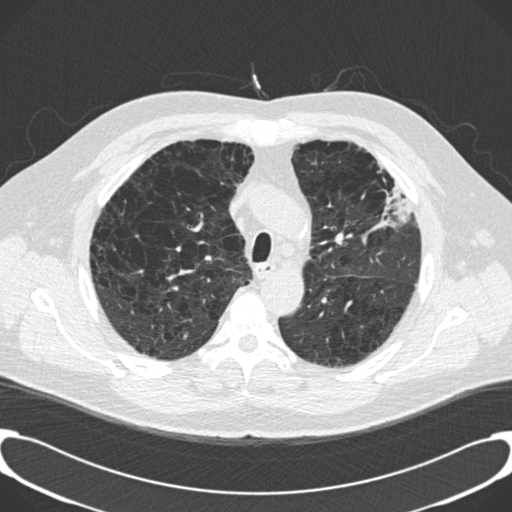
Axial slice from a low-dose chest CT screening exam; third screening round (two years after baseline); lung window (W 1500 / L -600 HU). Male participant, aged 59 years at enrolment. Current smoker at enrolment.
Expert reader's lesion annotation, box from (x=359, y=157) to (x=416, y=223) px. No non-calcified nodule or mass ≥4 mm was recorded by the screening reader at this exam. Official screen result: positive, other.